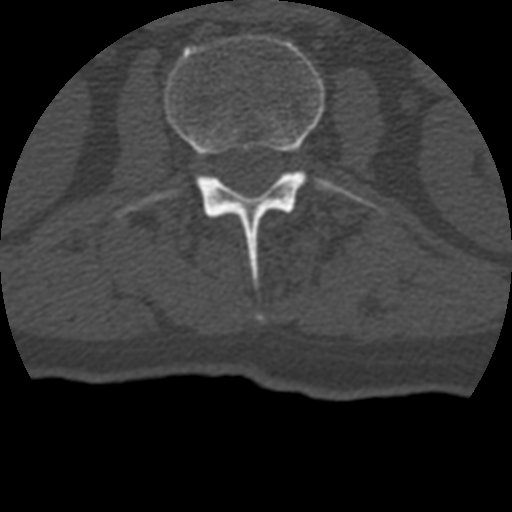
CT including the spine, one axial slice; bone window (W 1800 / L 400 HU); 1.25 mm slice thickness; 512 × 512 image matrix, field of view 160 × 160 mm. Patient age 69 years. From the clinical record (not read from this slice): primary cancer: prostate.
Structures marked on this image (semi-automatic segmentation, software-assisted and operator-edited):
- L2 vertebra: bounding box [x1, y1, x2, y2] px = [118, 34, 368, 280]